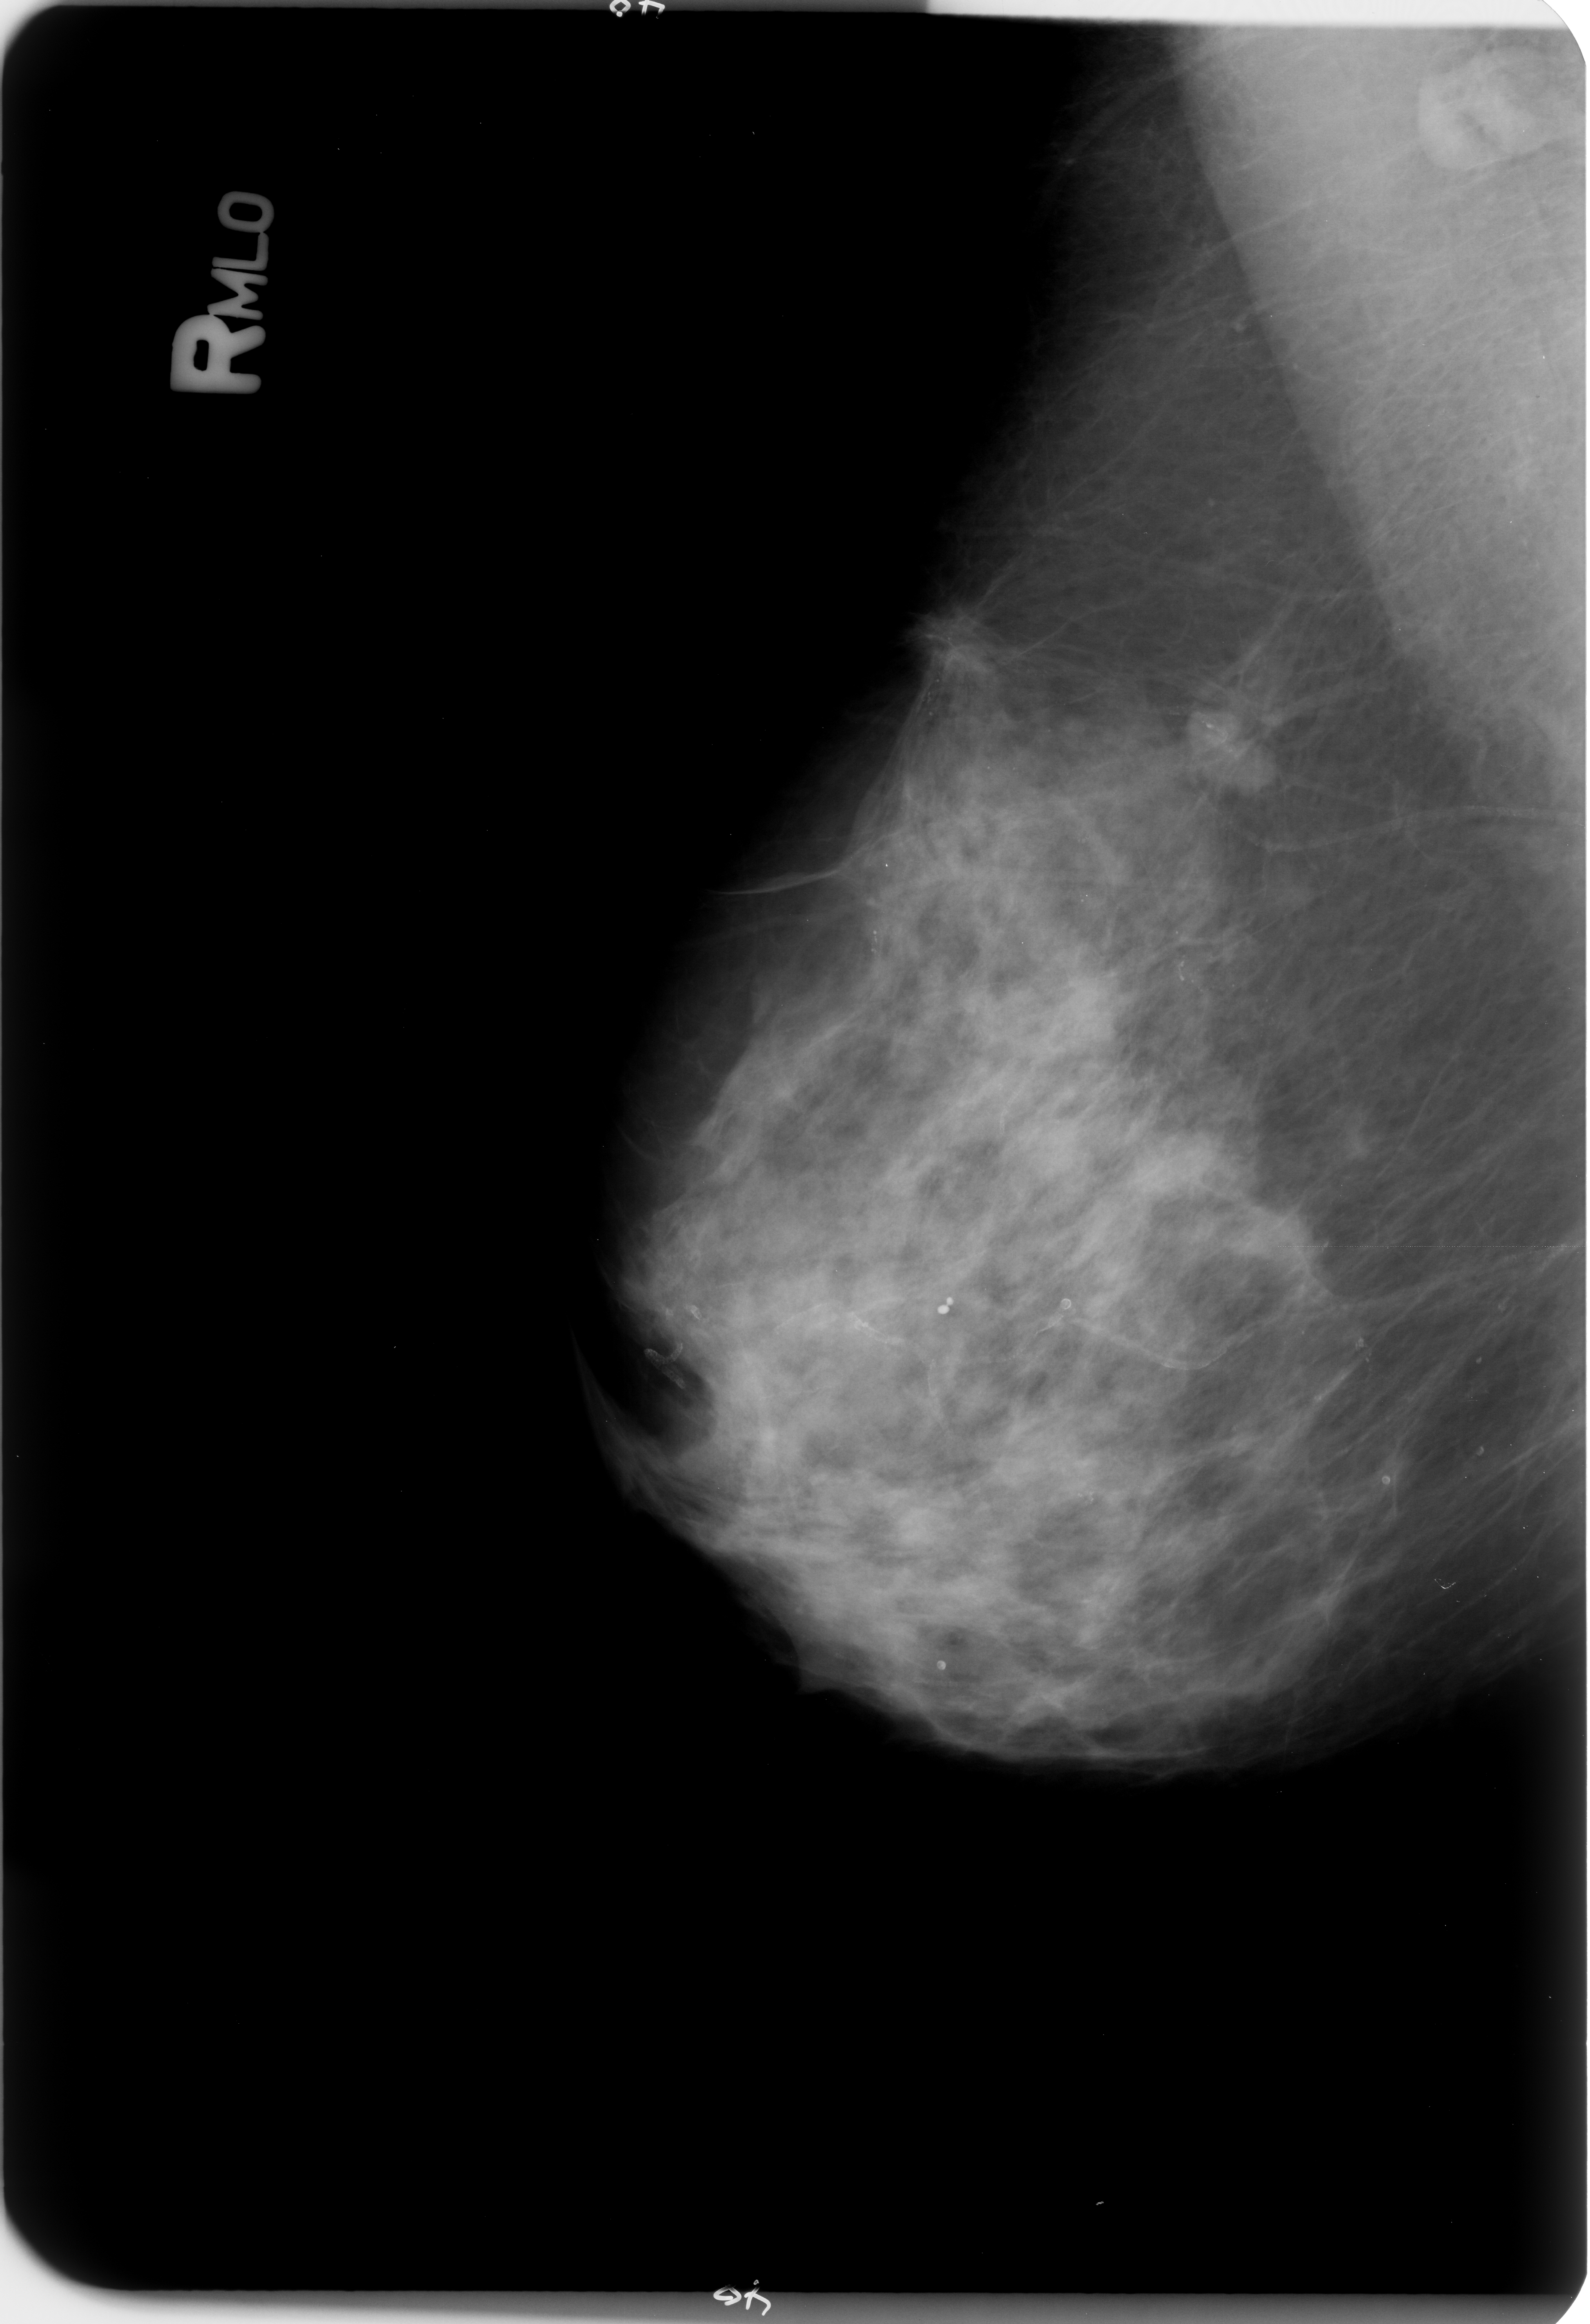
Mammogram (digitized film), right breast, MLO view, breast composition: heterogeneously dense (BI-RADS density category 3 of 4).
- Abnormality record for this image: Finding 1 of 2: mass, shape architectural distortion, margins ill defined / spiculated; BI-RADS assessment category 4; subtlety rating 4 on a 1 (subtle) to 5 (obvious) scale; pathology result (as recorded, not read from the image): malignant.
- Finding 2 of 2: mass, shape architectural distortion, margins ill defined / spiculated; BI-RADS assessment category 4; subtlety rating 4 on a 1 (subtle) to 5 (obvious) scale; pathology result (as recorded, not read from the image): malignant.